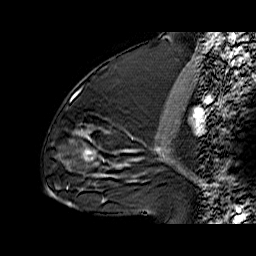
Breast MRI (dynamic contrast-enhanced), one sagittal slice; position 32 of 60 along the scan axis; dynamic contrast-enhanced series, time point 2 of 6 at this slice position (early post-contrast); 1.5 T; TE 6.3 ms, TR 32.9 ms; 4 mm slice thickness; 256 × 256 image matrix. Female patient. Case-level facts recorded for this patient, not image findings: setting: breast cancer imaged before/during neoadjuvant chemotherapy; receptor status: triple-negative.
Outlined on this slice (semi-automatically segmented with operator editing):
- analysis volume of interest (the breast-tissue region the enhancement analysis was run in; not a lesion): bounding box <55,76,126,170> (left, top, right, bottom; pixels)
- tumour enhancement mask (voxels above the 100 % enhancement threshold inside the analysis volume of interest): <78,131,116,155>